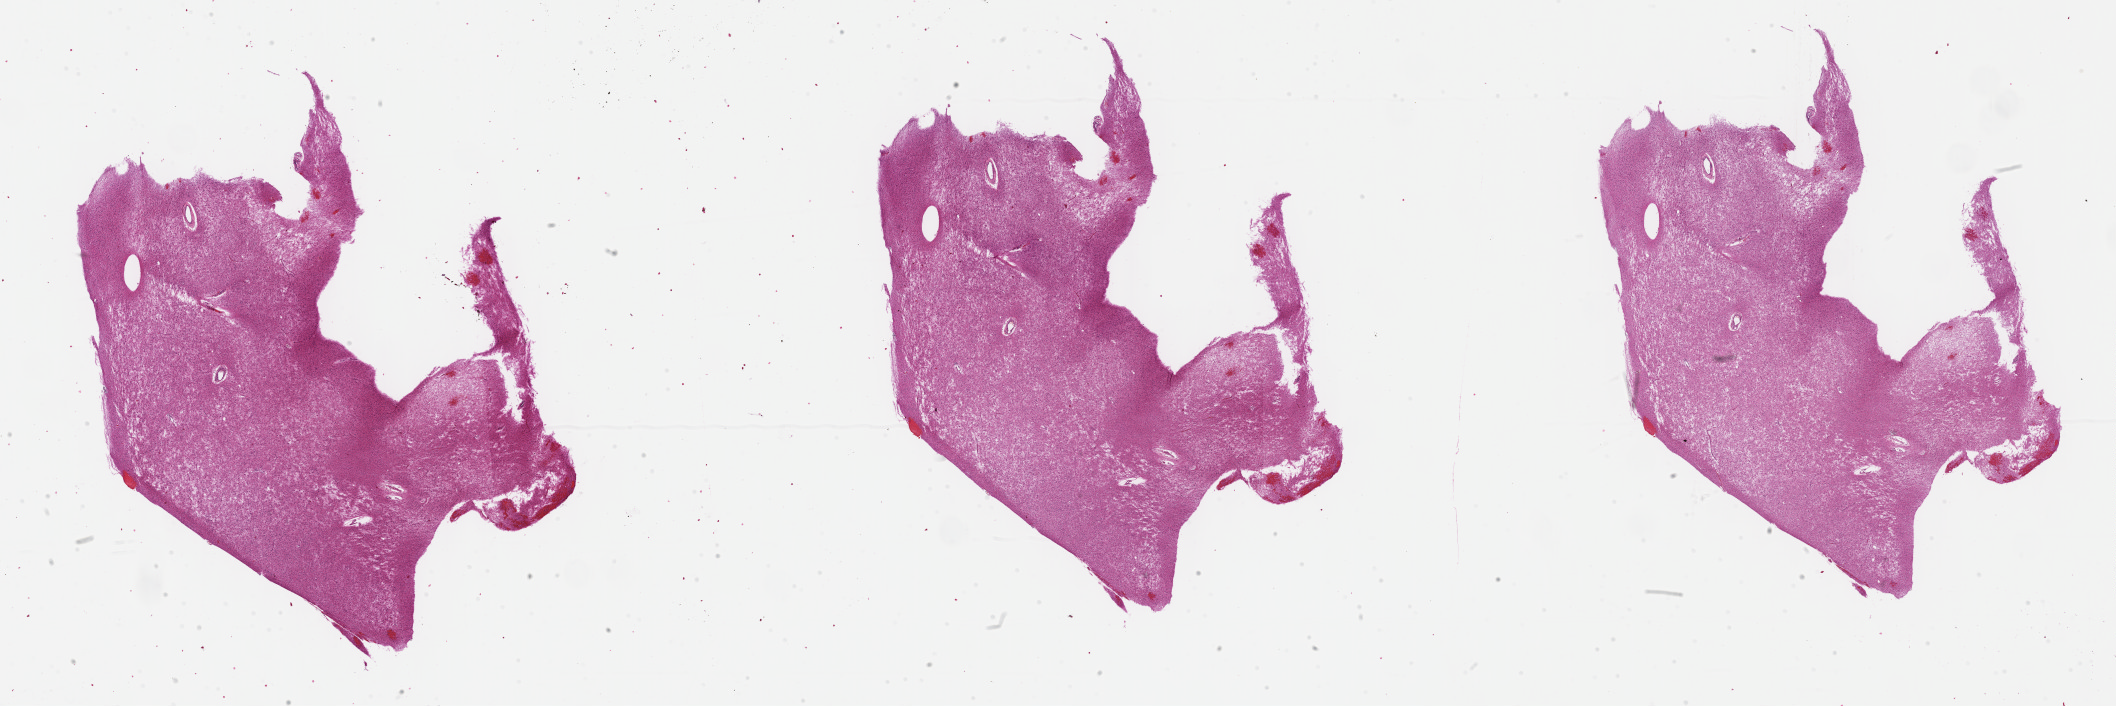
H&E whole-slide image — shown as a low-resolution overview of the whole scanned area (about 34.2 x 11.4 mm, acquisition: 40x scan), formalin-fixed paraffin-embedded (FFPE) diagnostic section, sample: primary tumour, brain. Male patient; age at initial diagnosis 60 years. Histologic grade: G2 (moderately differentiated).
- diagnosis: Mixed glioma (cerebrum)
- laterality: right